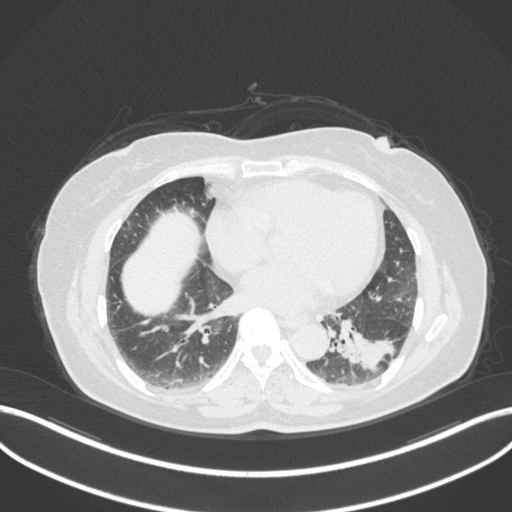
Chest CT, one axial slice. Reconstruction kernel B31f. 120 kVp. Lung window (W 1500 / L -600 HU). 512 × 512 image matrix. Patient: female, 59 years. Case-level facts recorded for this patient, not image findings: clinical TNM (as recorded): T2a N0 M0.
Structures marked on this image (rectangle marked by the reading radiologist):
- lung tumour (recorded histology: adenocarcinoma): box from (x=329, y=318) to (x=398, y=377) px